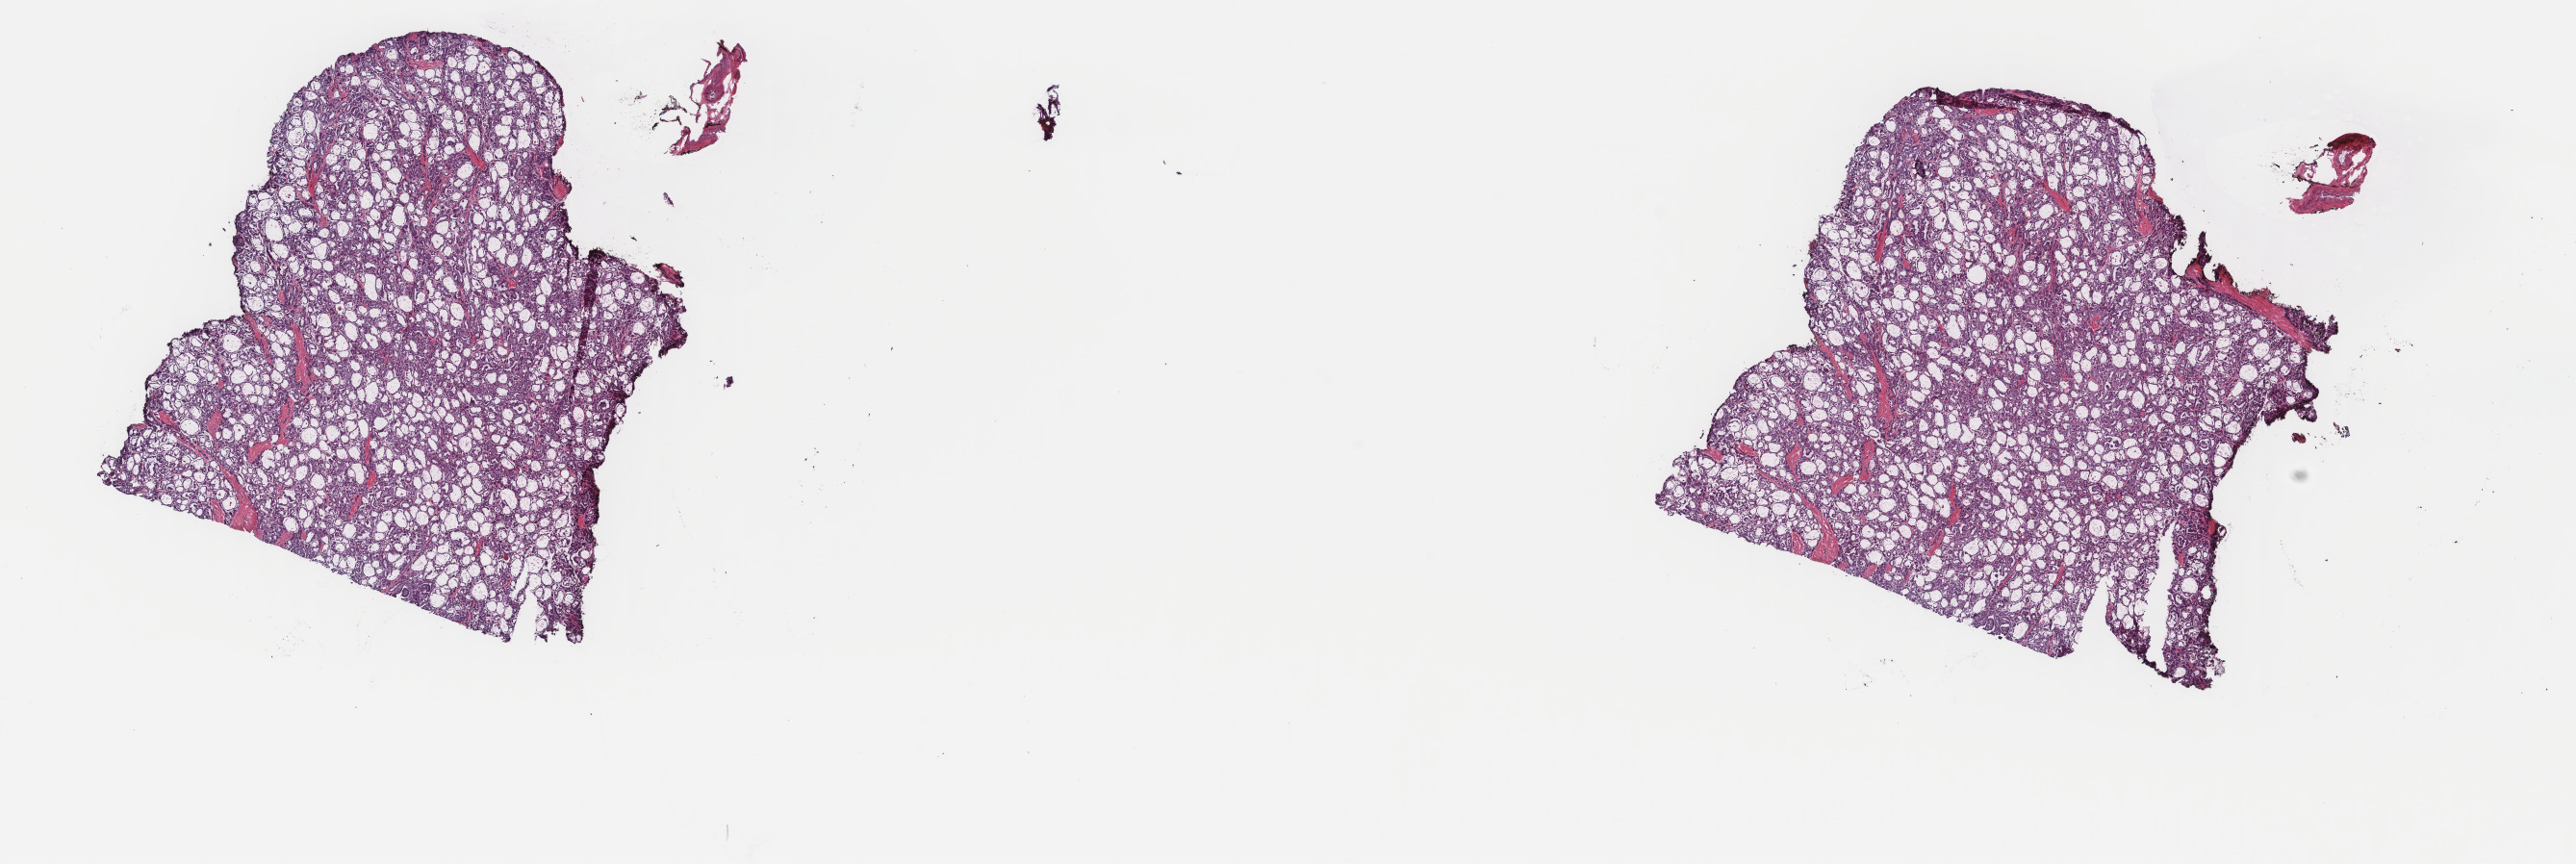
Whole-slide histology image, Hematoxylin and eosin (H&E) stained, shown as a low-resolution overview of the whole scanned area (about 21.2 x 7.1 mm), frozen section from the top of the tissue portion, primary tumour sample from the thyroid. Patient: female, age at initial diagnosis 49 years. Slide review estimates, as recorded: tumour cells 90%, tumour nuclei 100%, normal cells 0%, stromal cells 10%, necrosis 0%. Inflammatory infiltration, as recorded: lymphocyte infiltration 0%, monocyte infiltration 0%, neutrophil infiltration 0%.
- lymph nodes positive (case pathology): 5 of 9 examined
- laterality: left
- pathologic diagnosis: Papillary adenocarcinoma, NOS (thyroid gland)
- TNM: T3 N1b M0
- AJCC pathologic stage: IVA